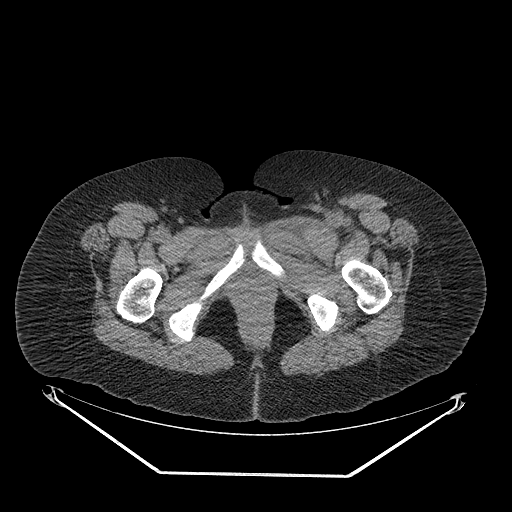
CT of an extremity soft-tissue mass (from a PET/CT study), one axial slice; position 49 of 267 along the scan axis; 140 kVp; soft-tissue window (W 400 / L 40 HU); 512 × 512 image matrix, field of view 500 × 500 mm. Female patient. From the clinical record (not read from this slice): histological type: myxofibrosarcoma; grade: intermediate; site of the primary tumour: left thigh.
Outlined on this slice (expert contour drawn on MRI and transferred to this co-registered scan by the dataset authors):
- gross tumour volume including surrounding oedema: box from (x=267, y=208) to (x=360, y=250) px